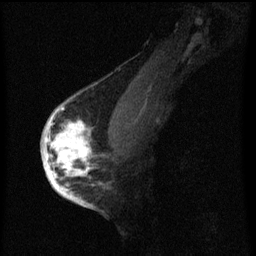
Breast MRI (dynamic contrast-enhanced), one sagittal slice. Position 40 of 60 along the scan axis. Dynamic contrast-enhanced series, image 2 of 3 at this slice position (ordered by acquisition). 1.5 T. TE 4.2 ms, TR 8 ms. 256 × 256 image matrix, field of view 180 × 180 mm. Female patient, age 56 years.
Annotated regions visible in this slice (semi-automatically segmented with operator editing):
- analysis volume of interest (the breast-tissue region the enhancement analysis was run in; not a lesion): bounding box <42,110,107,193> (left, top, right, bottom; pixels)
- tumour enhancement mask (voxels above the 70 % enhancement threshold inside the analysis volume of interest): <42,110,91,193>